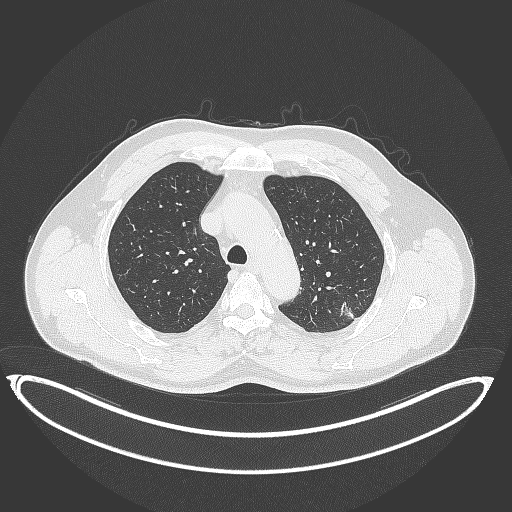
Chest CT, one axial slice. Position 273 of 399 along the scan axis. Reconstruction kernel B70f. Lung window (W 1500 / L -600 HU). 1 mm slice thickness. 512 × 512 image matrix. Male patient, age 58 years. From the clinical record (not read from this slice): clinical TNM (as recorded): T1c N0 M0; histopathological grade: G1-2.
Structures marked on this image (rectangle marked by the reading radiologist):
- lung tumour (recorded histology: adenocarcinoma): bounding box <340,296,362,324> (left, top, right, bottom; pixels)